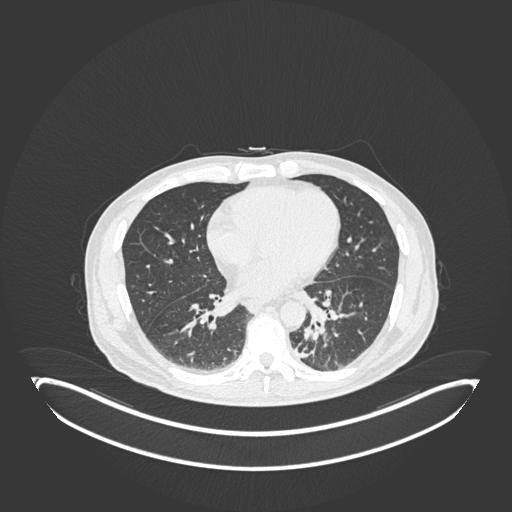
Chest CT, one axial slice; position 64 of 251 along the scan axis; reconstruction kernel B30f; 120 kVp; lung window (W 1500 / L -600 HU); 1 mm slice thickness; 512 × 512 image matrix, field of view 500 × 500 mm. Male patient, age 72 years. From the clinical record (not read from this slice): clinical TNM (as recorded): T2b N0 M1.
Outlined on this slice (bounding box drawn by a radiologist):
- lung tumour (recorded histology: adenocarcinoma): box from (x=294, y=323) to (x=321, y=362) px